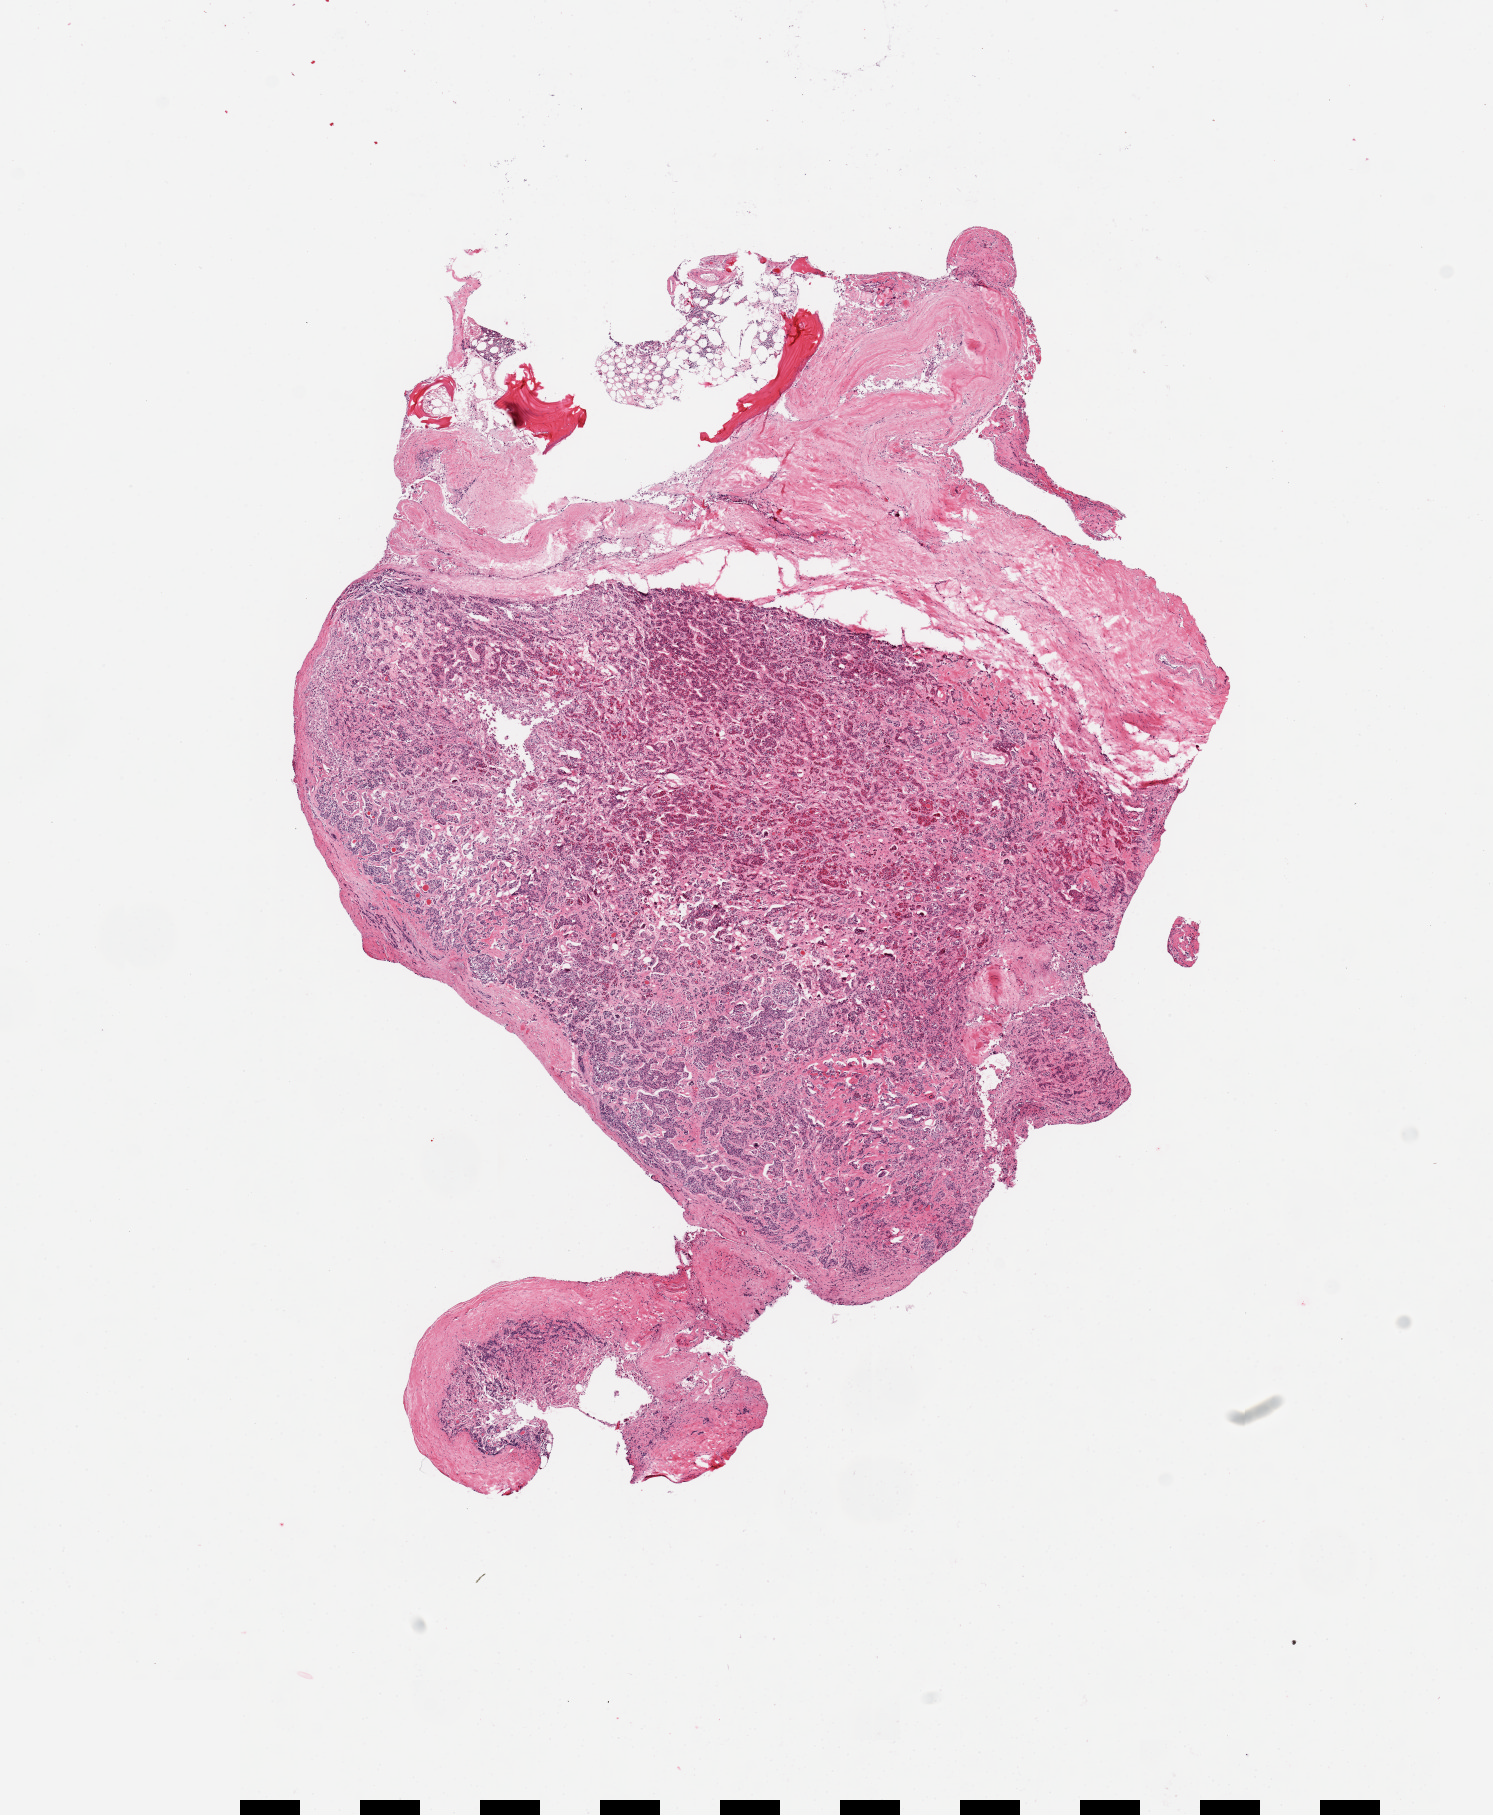
Whole-slide image, H&E stain, brightfield, shown as a low-resolution overview of the whole scanned area (about 11.8 x 14.4 mm). PAXgene-fixed, paraffin-embedded tissue. Target tissue: pituitary. Donor tissue sample. Male donor.
- review note (as recorded): 1 piece; fragment of bone and bone marrow, dura and adenohypophysis